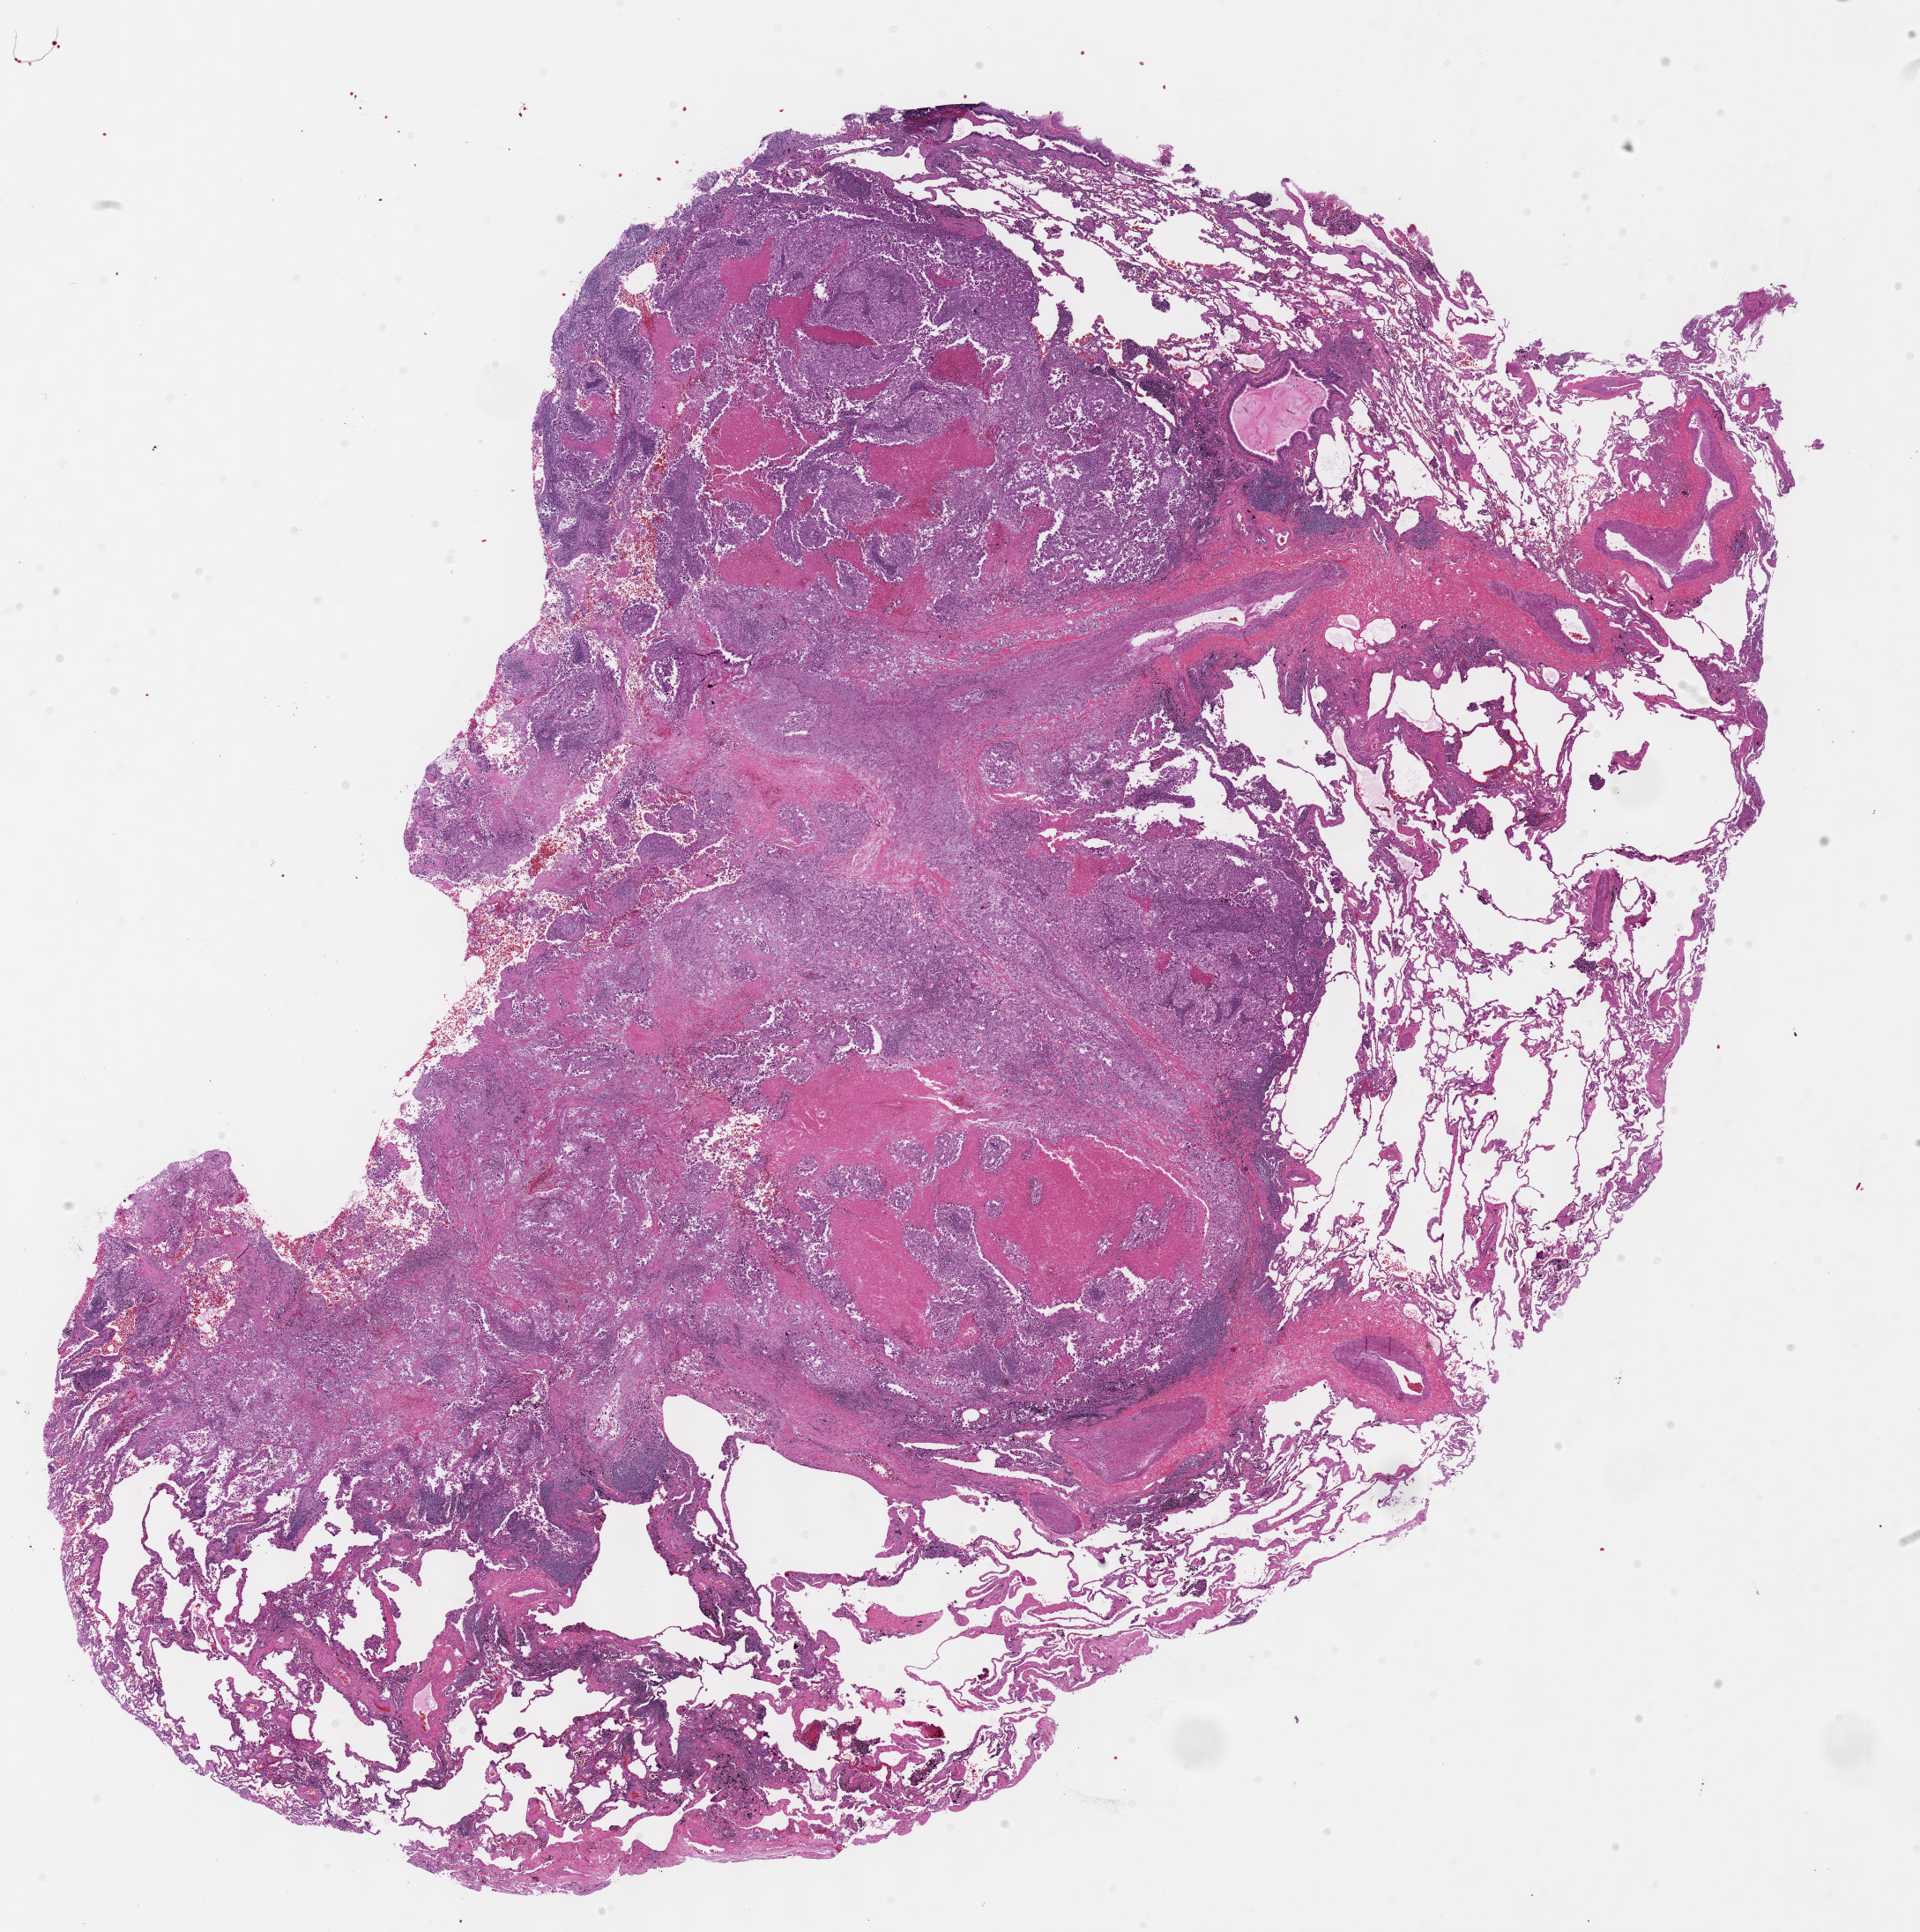
Digitized H&E tissue section (whole slide) — whole scanned area (about 17.6 x 17.7 mm, slide scanned at 40x) shown as a low-resolution overview; FFPE section; lung, primary tumour sample. Female, age 51 years at initial diagnosis.
• TNM: T1 N0 MX
• AJCC pathologic stage: IA
• histologic diagnosis: Adenocarcinoma, NOS (upper lobe, lung)